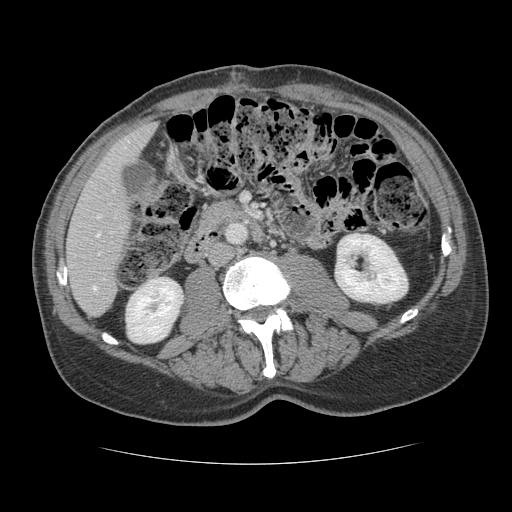
Contrast-enhanced abdominal CT, one axial slice. Slice 42 of 134 in the series (ordered by position). 120 kVp. Soft-tissue window (W 400 / L 40 HU). 512 × 512 image matrix, field of view 377 × 377 mm. Male patient, age 68 years. Case-level facts recorded for this patient, not image findings: diagnosis: colorectal cancer liver metastases, imaged before liver resection; multiple liver metastases: yes; largest metastasis: 2.2 cm; chemotherapy before resection: no.
Annotated regions visible in this slice (outlined manually by an expert reader):
- hepatic veins: box from (x=96, y=215) to (x=100, y=237) px
- liver: (x=67, y=124)–(x=154, y=316)
- planned liver remnant (the part of the liver to remain after resection): (x=67, y=124)–(x=154, y=316)
- portal vein (with intrahepatic branches): (x=93, y=253)–(x=100, y=290)